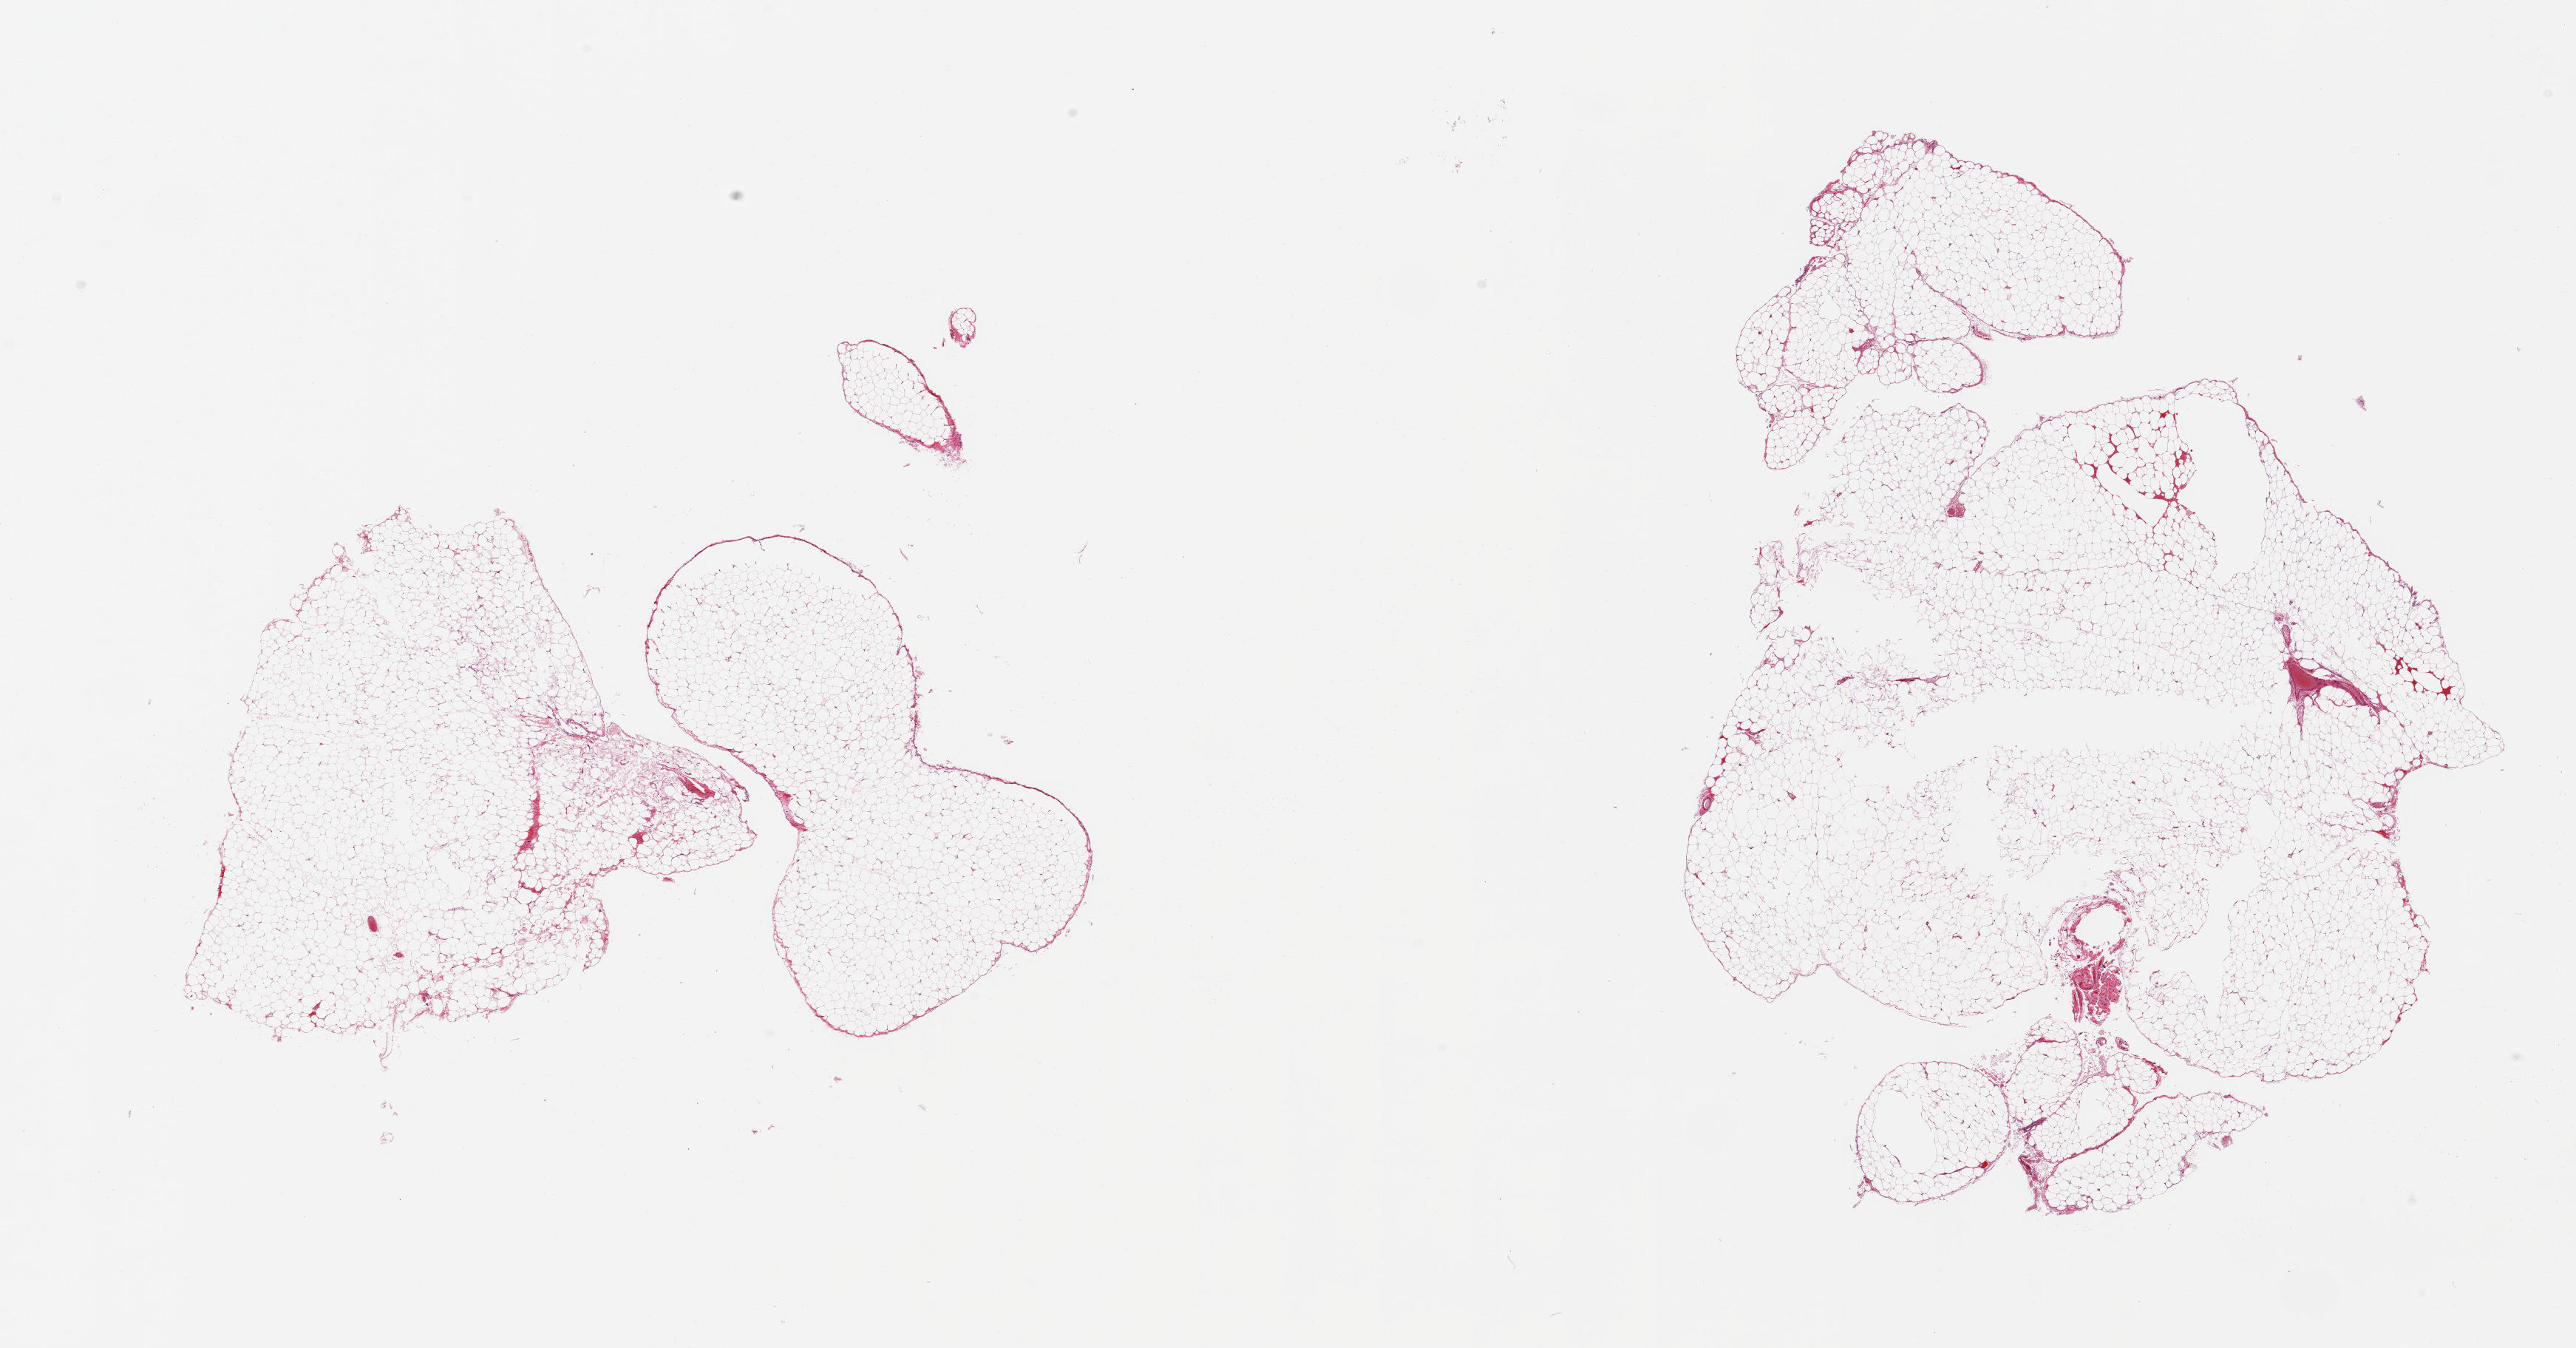
Whole-slide image, H&E stain, a low-resolution overview of the entire scanned area, about 27.6 x 14.4 mm, PAXgene-fixed paraffin-embedded (PFPE) section, sampled site (target tissue): omentum, tissue donor sample. Donor: male.
Review note (as recorded): 2 pieces; mature fat.